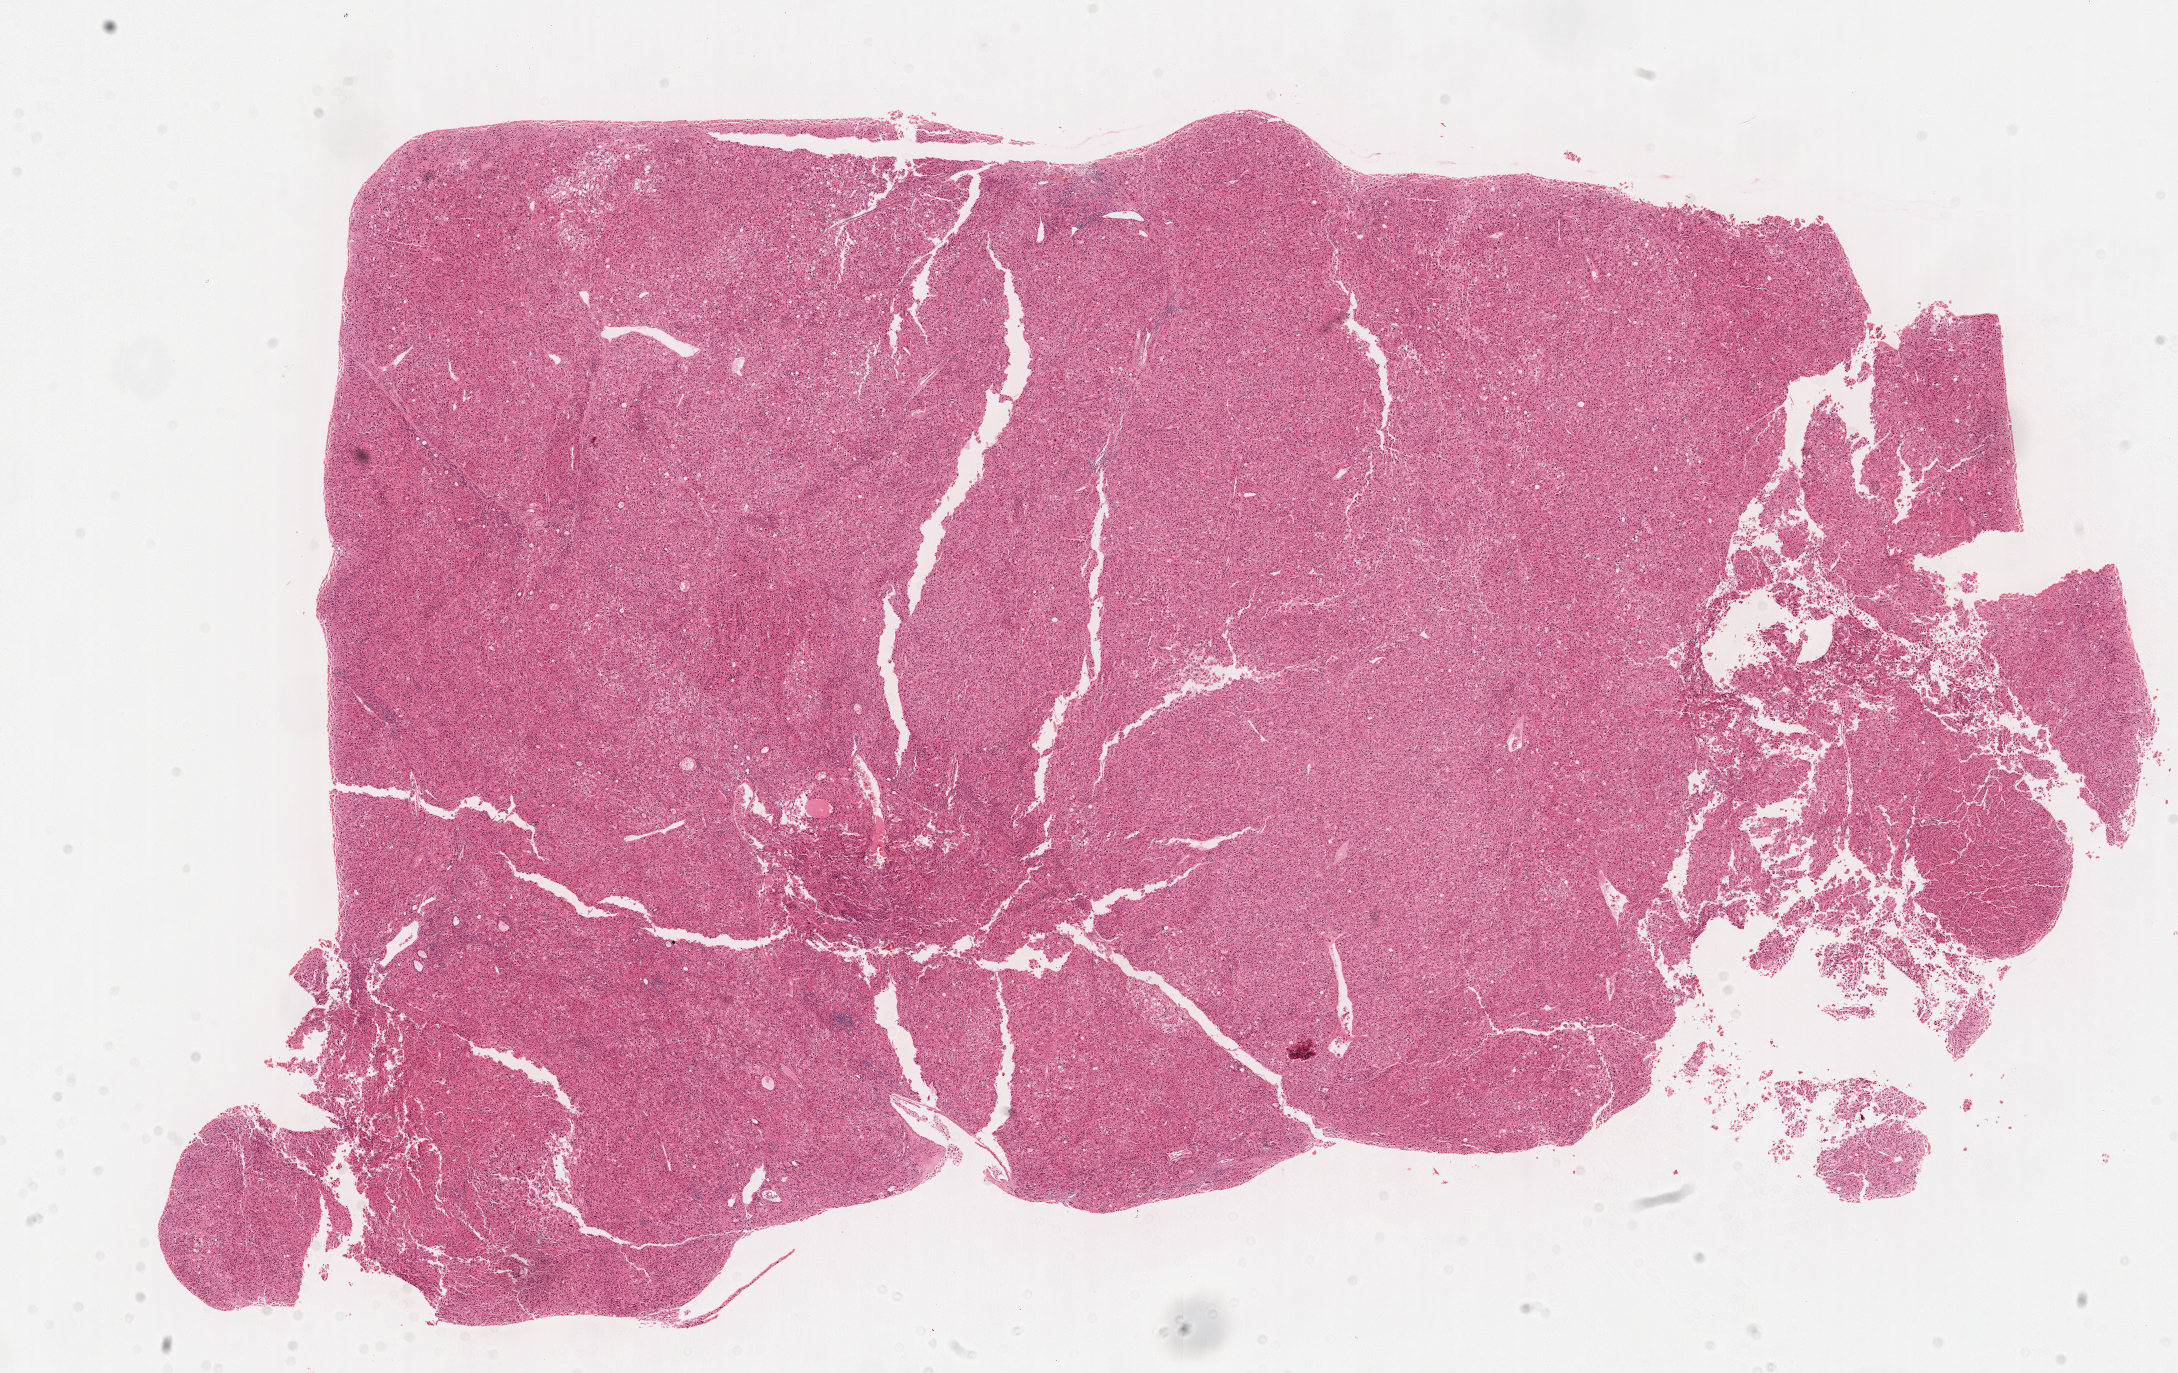
H&E-stained whole-slide image — a low-resolution overview of the entire scanned area, about 17.6 x 11.1 mm (acquisition: 40x scan); formalin-fixed paraffin-embedded (FFPE) diagnostic section; liver, primary tumour sample. Patient: male, age at initial diagnosis 62 years. Histologic grade: G3 (poorly differentiated).
AJCC pathologic stage: I (6th edition). Diagnosis: Hepatocellular carcinoma, NOS.